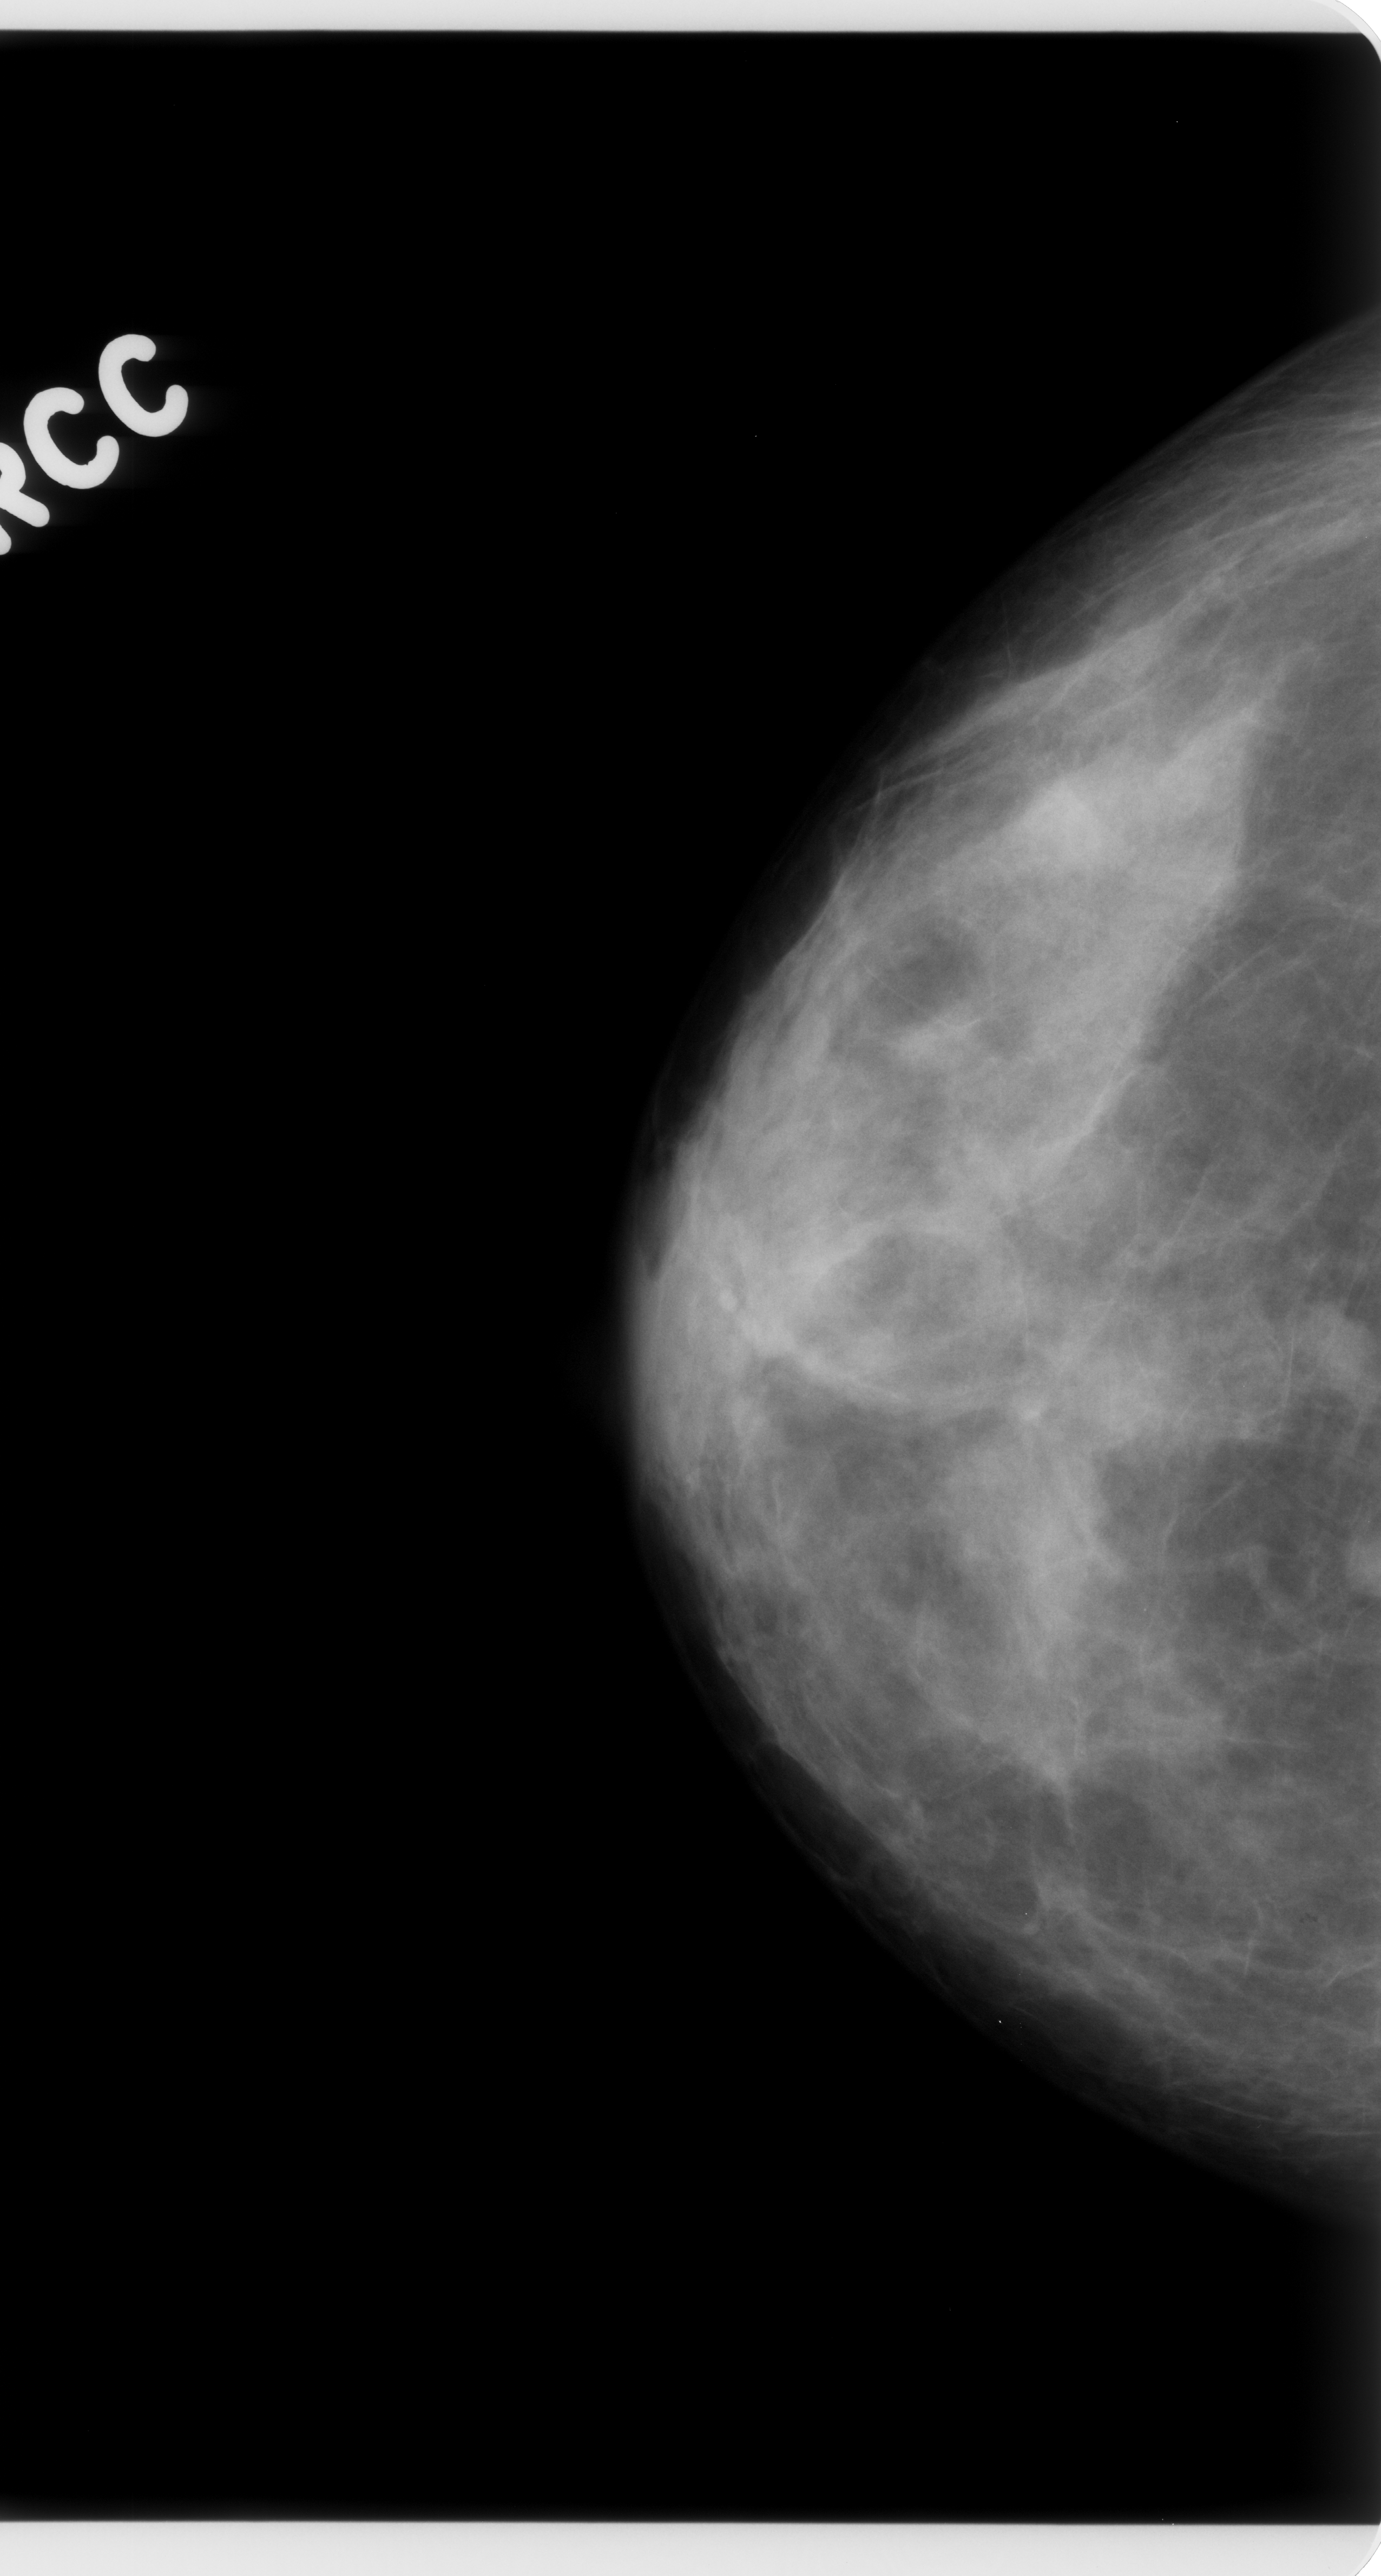
Mammogram (digitized film); right breast; CC view.
Abnormality record for this image: mass, shape round, margins circumscribed; BI-RADS assessment category 4; pathology result (as recorded, not read from the image): malignant.